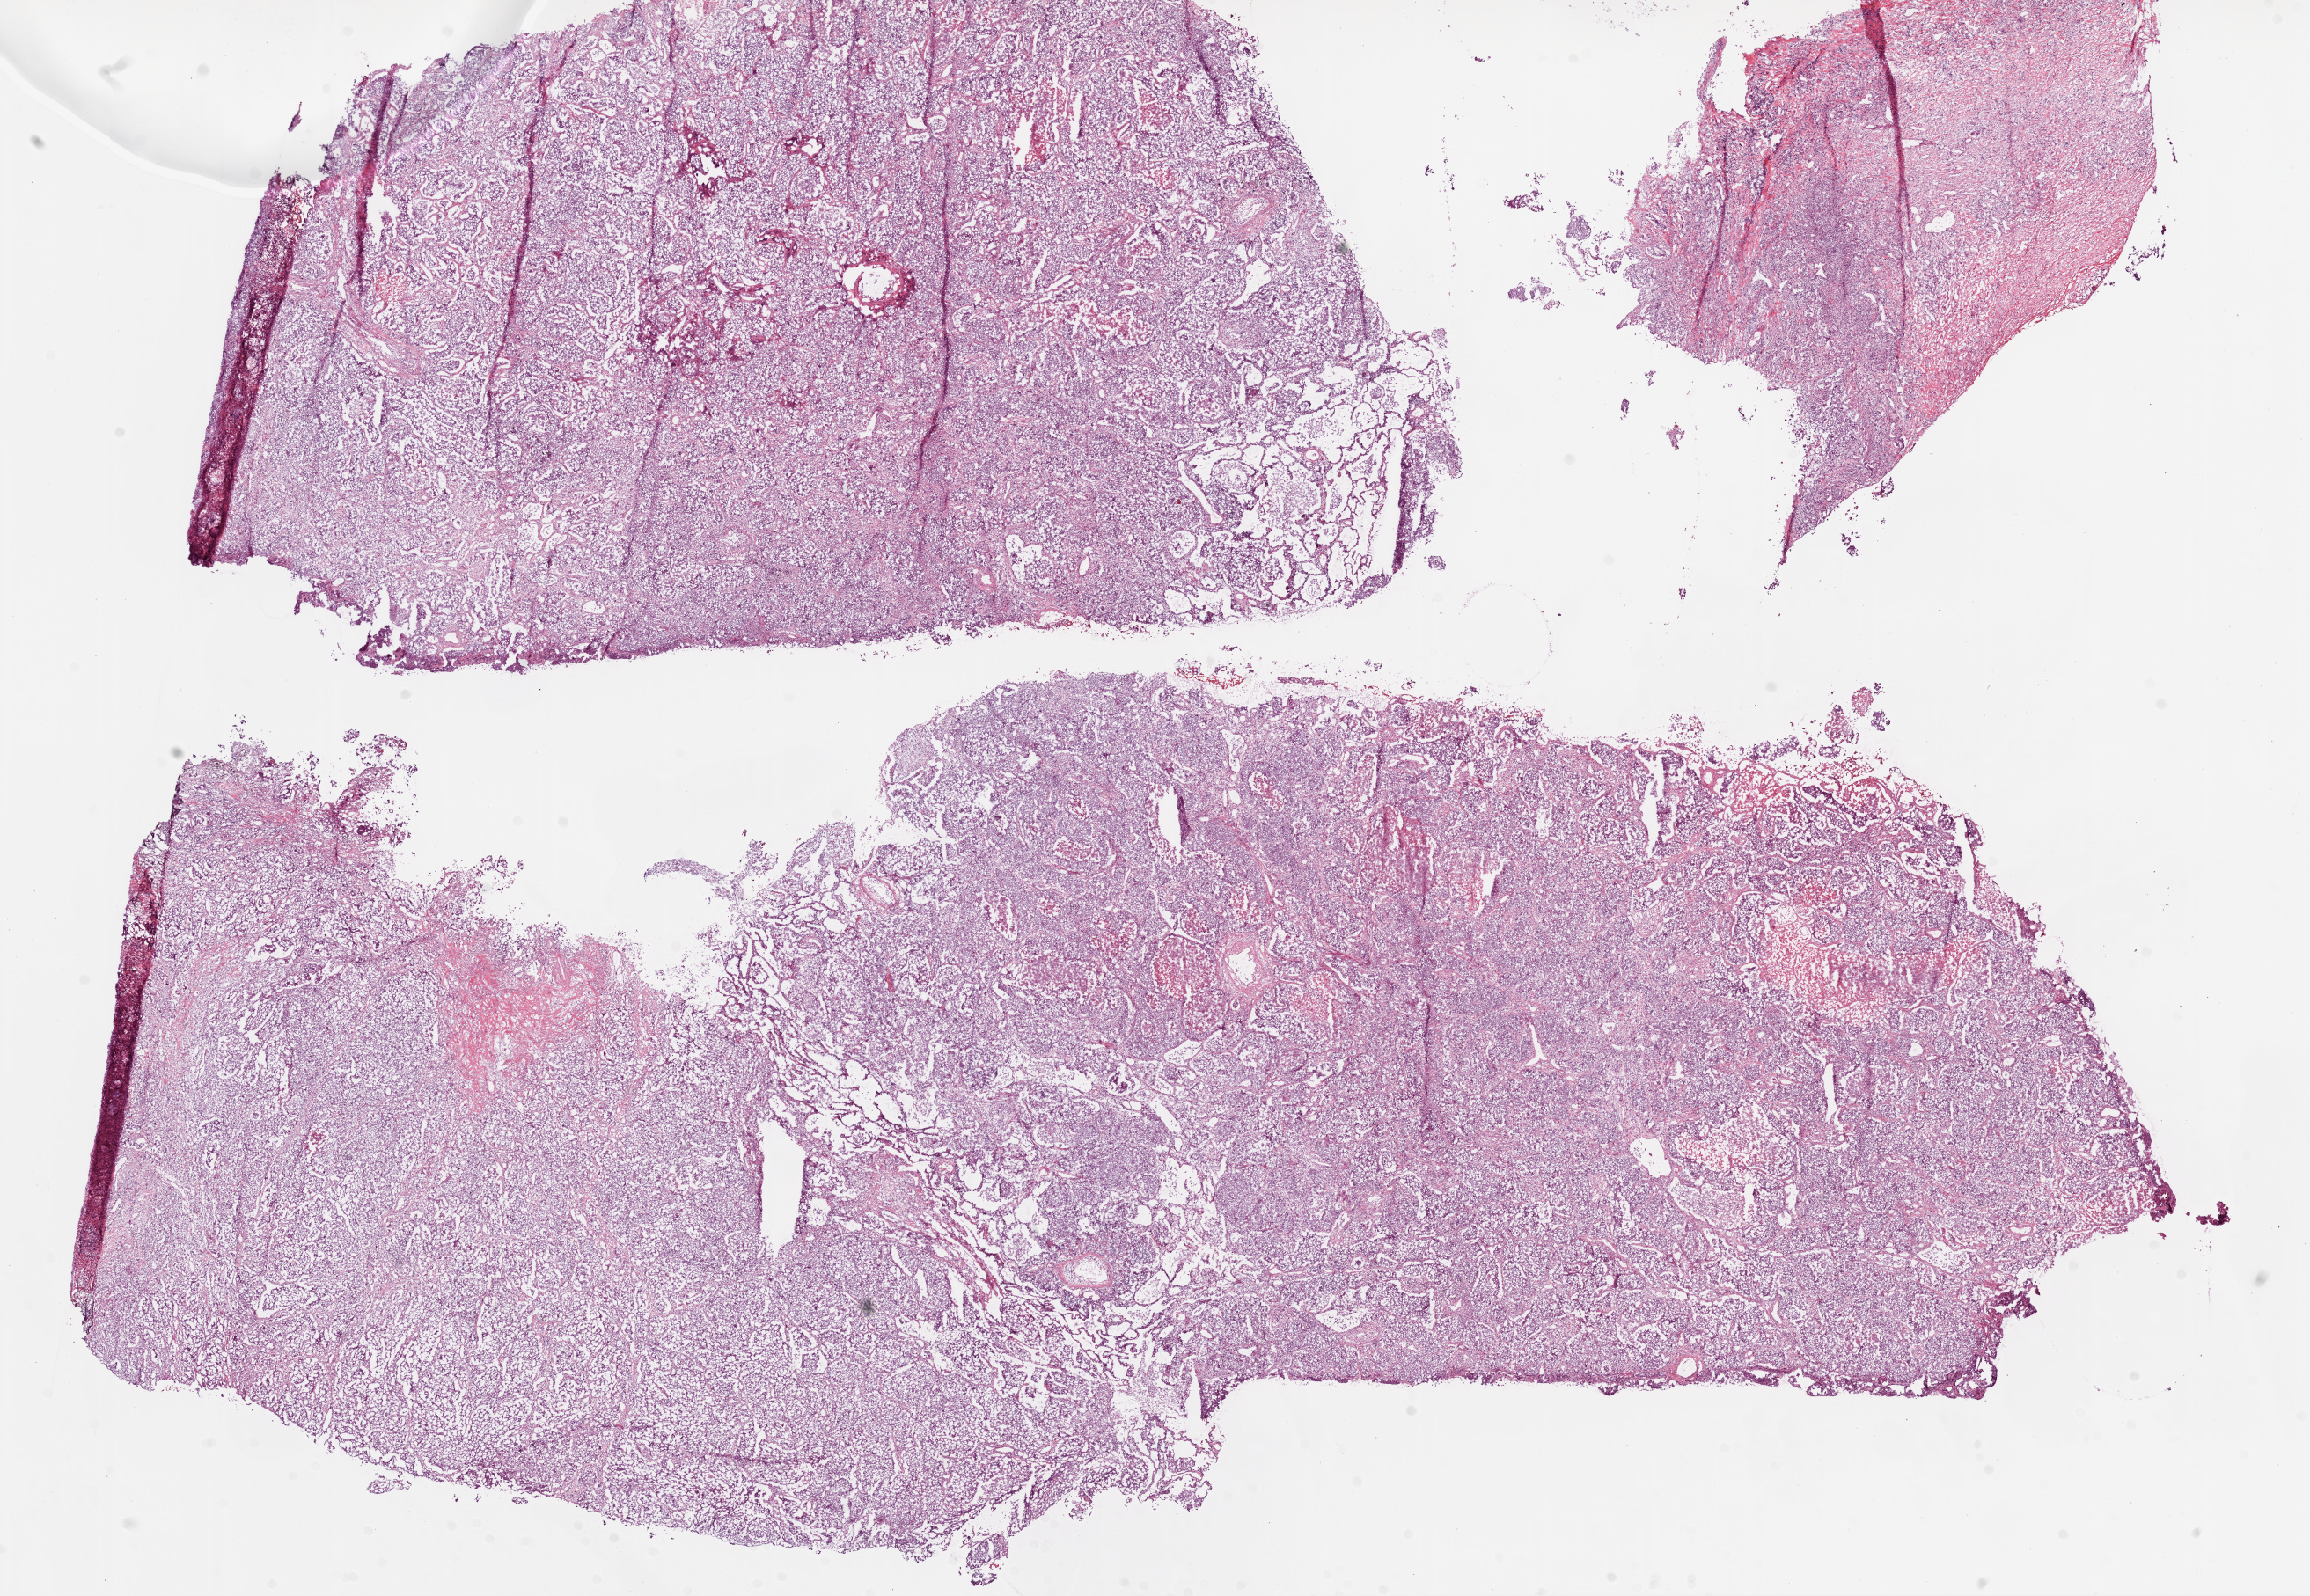
Digitized H&E tissue section (whole slide) — low-resolution overview of the scanned area, about 21.1 x 14.6 mm. Frozen section from the top of the tissue portion. Primary tumour sample from the lung. Female, age 70 years at initial diagnosis. Composition of this section per pathologist review: tumour cells 88%, tumour nuclei 80%, normal cells 2%, stromal cells 6%, necrosis 4%. Infiltration values recorded for this section: lymphocyte infiltration 10%, monocyte infiltration 2%.
- pathologic diagnosis: Squamous cell carcinoma, NOS
- AJCC pathologic stage: IA (6th edition)